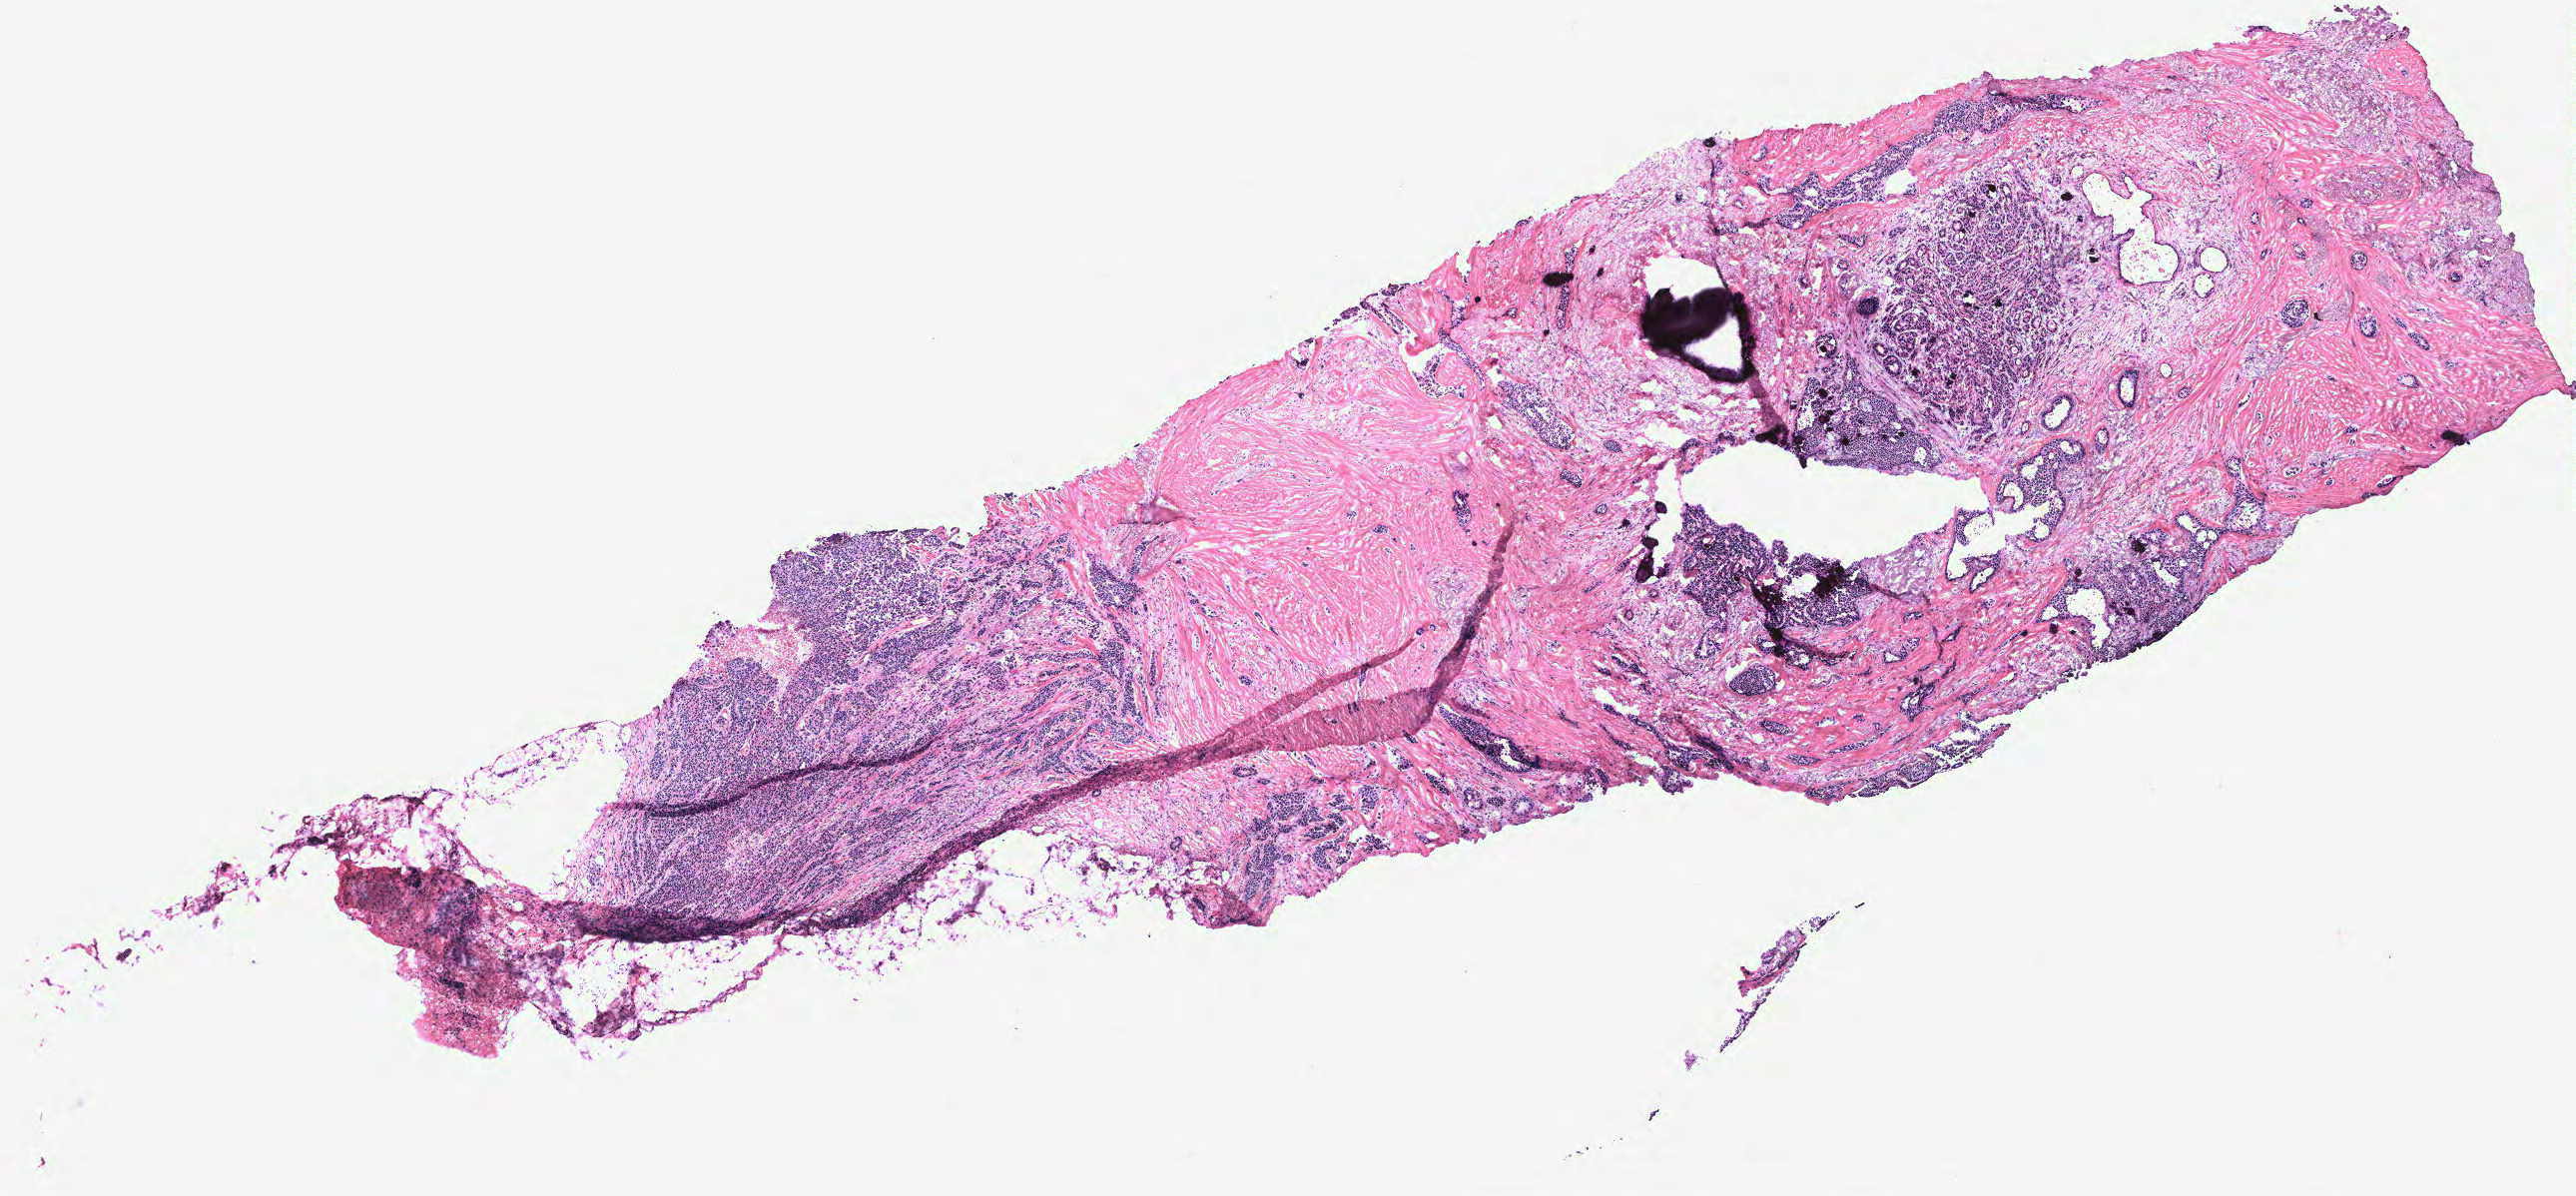
Whole-slide histology image, H&E-stained — whole scanned area (about 10.3 x 4.8 mm) shown as a low-resolution overview; breast, tumour tissue. Female, 59 y/o.
AJCC pathologic stage: IIA. Histologic diagnosis: Infiltrating duct carcinoma, NOS.